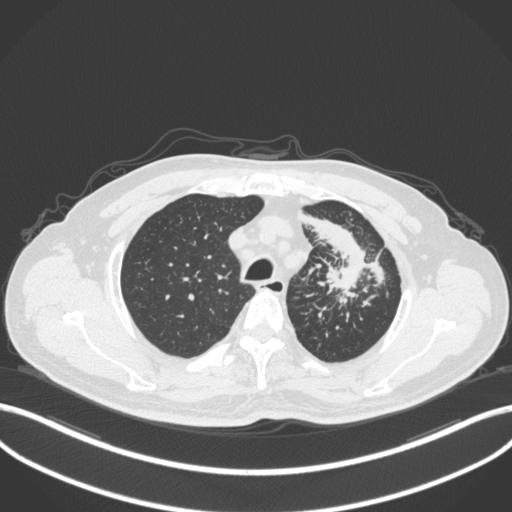
Chest CT, one axial slice; slice 285 of 386 in the series (ordered by position); reconstruction kernel B31f; 120 kVp; lung window (W 1500 / L -600 HU); 512 × 512 image matrix, field of view 400 × 400 mm. Patient: male, 69 years. From the clinical record (not read from this slice): clinical TNM (as recorded): T2a N2 M0.
Outlined on this slice (bounding box drawn by a radiologist):
- lung tumour (recorded histology: adenocarcinoma): box from (x=298, y=212) to (x=390, y=300) px